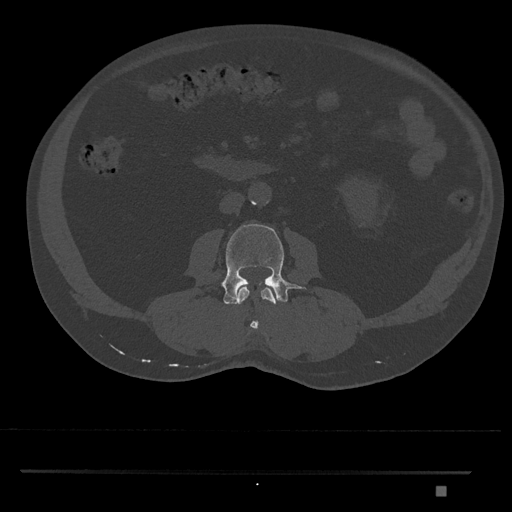
CT including the spine, one axial slice. Reconstruction kernel Br40s/3. Bone window (W 1800 / L 400 HU). 0.5 mm slice thickness. 512 × 512 image matrix, field of view 429 × 429 mm. Male patient, age 65 years. From the clinical record (not read from this slice): primary cancer: prostate.
Structures marked on this image (semi-automatic segmentation, software-assisted and operator-edited):
- L2 vertebra: bounding box <237,286,276,330> (left, top, right, bottom; pixels)
- L3 vertebra: <222,224,303,305>